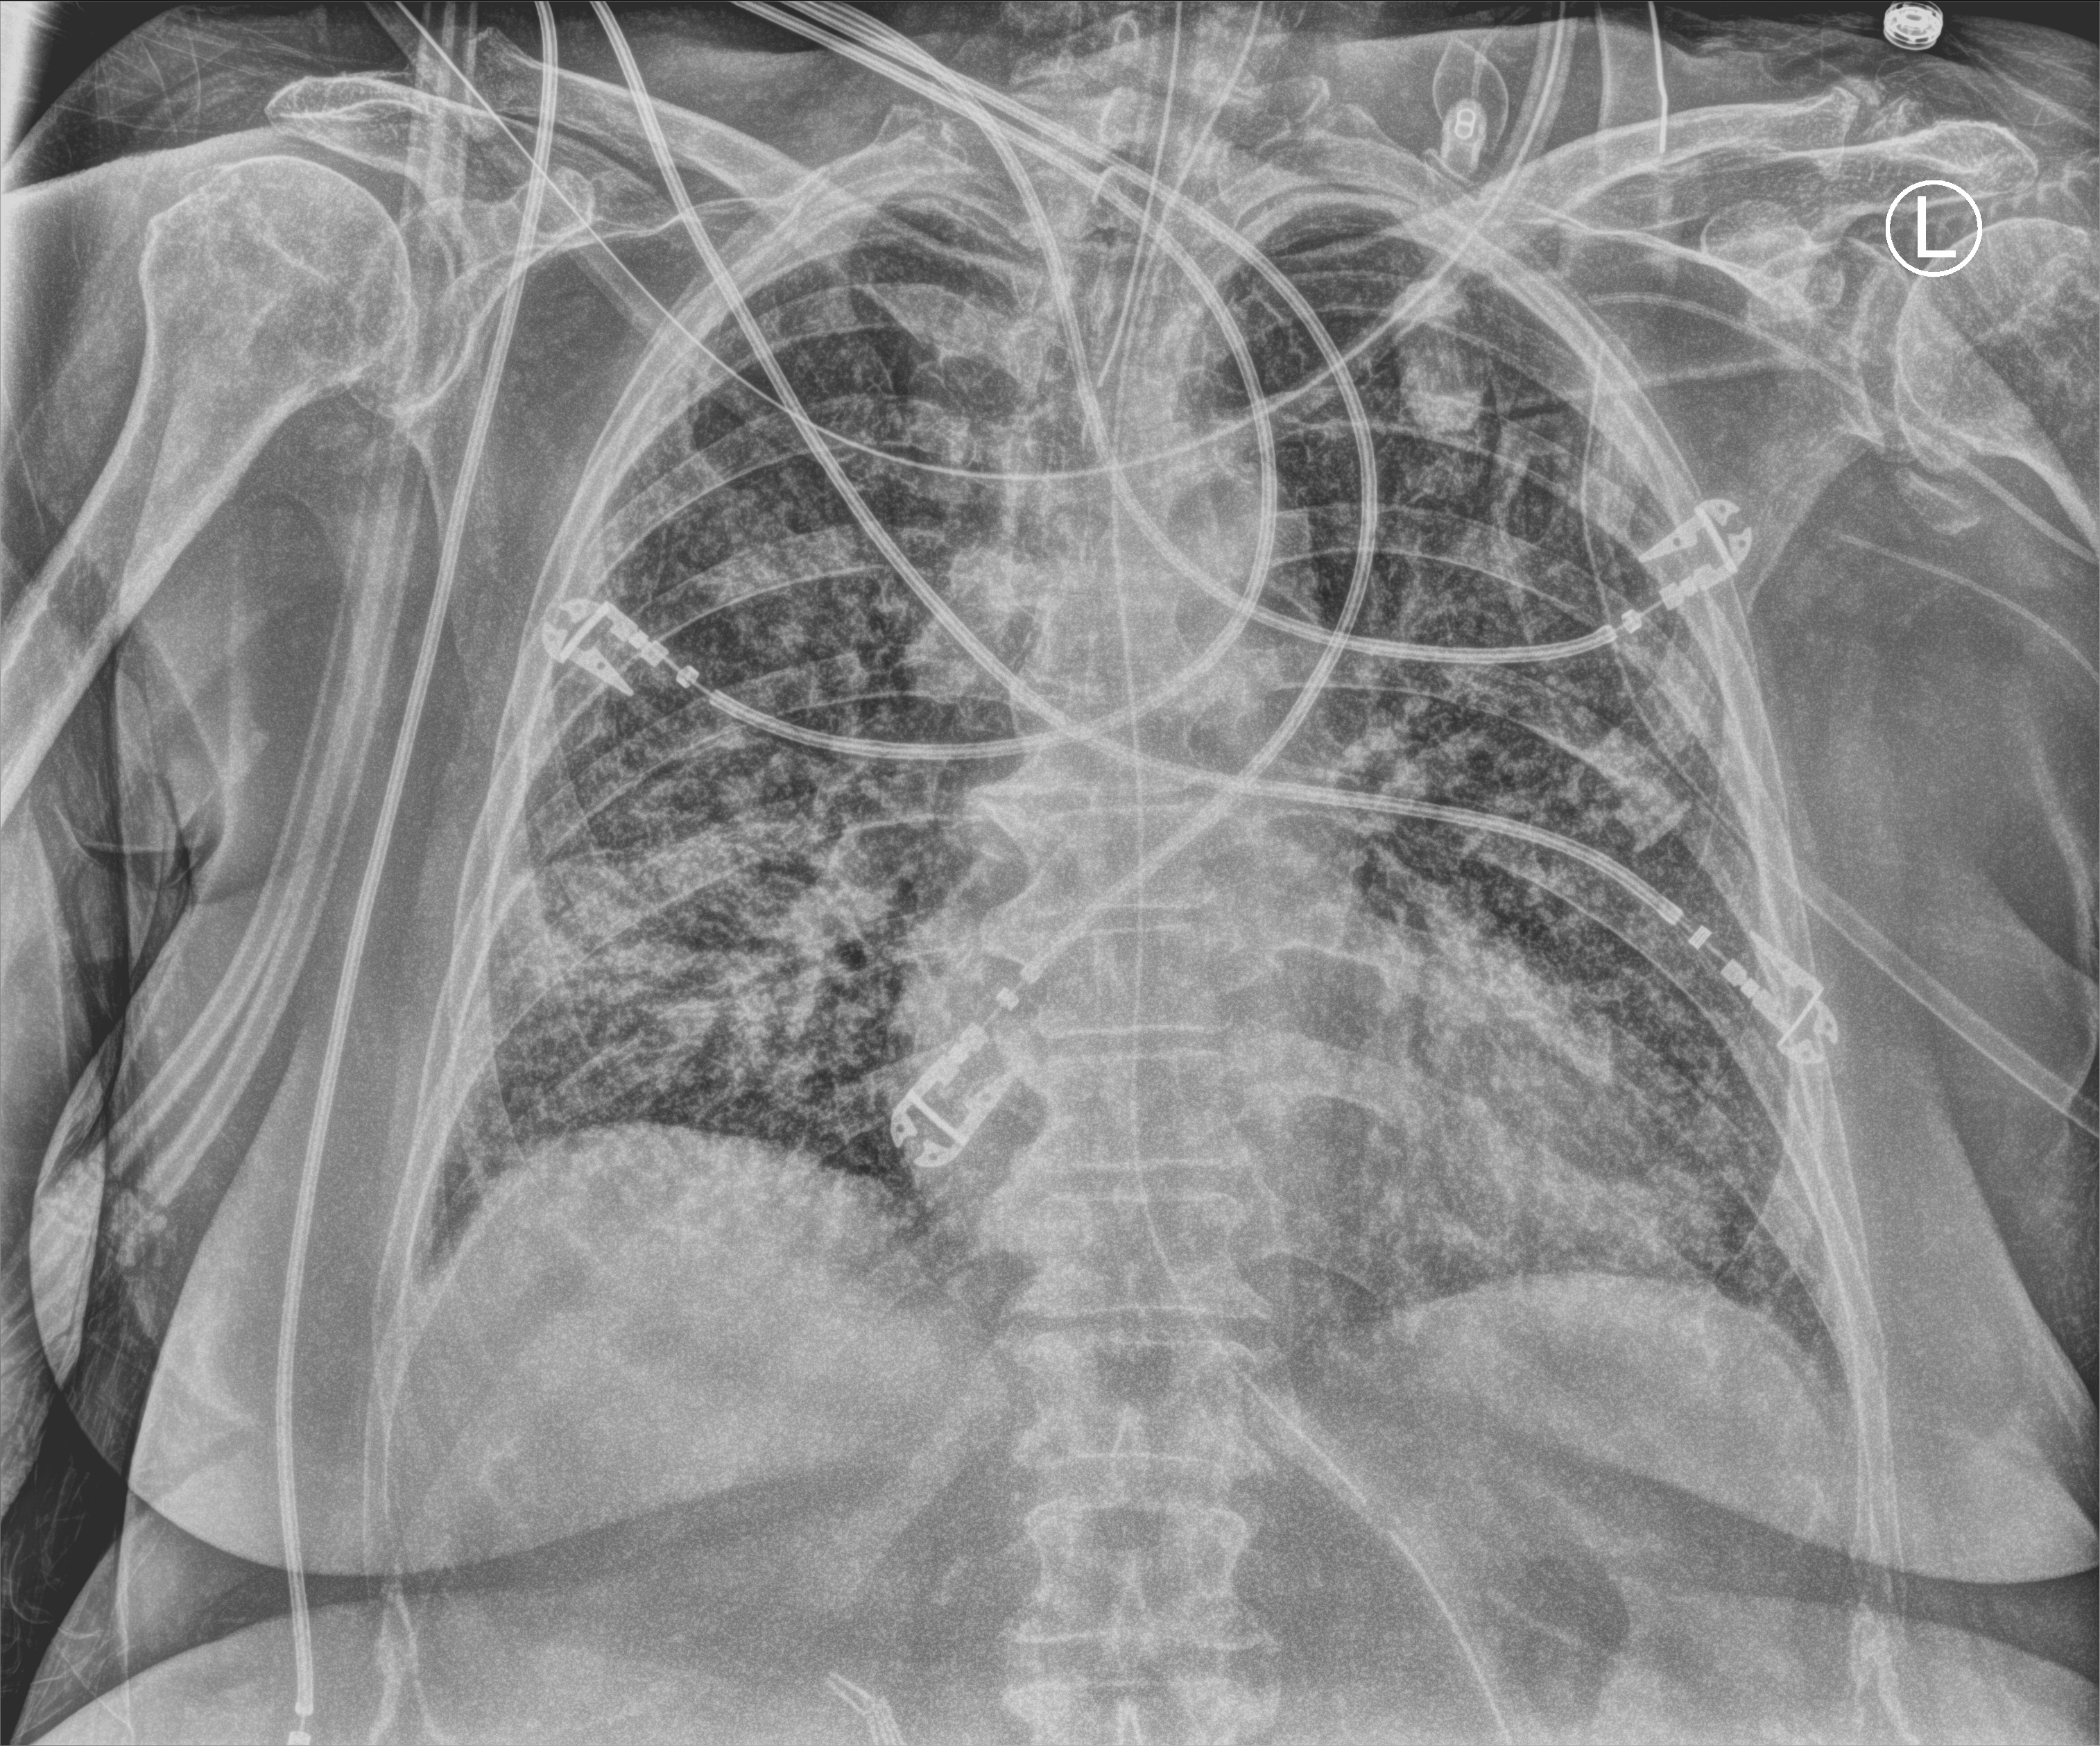
Chest X-ray (portable); anteroposterior (AP) projection. Female patient hospitalised with COVID-19, age 75–90 years.
Admission-level facts for this patient (not findings on this image; timing relative to this image not recorded): chronic kidney disease (admission record): no; admitted to intensive care during this hospital stay: no.